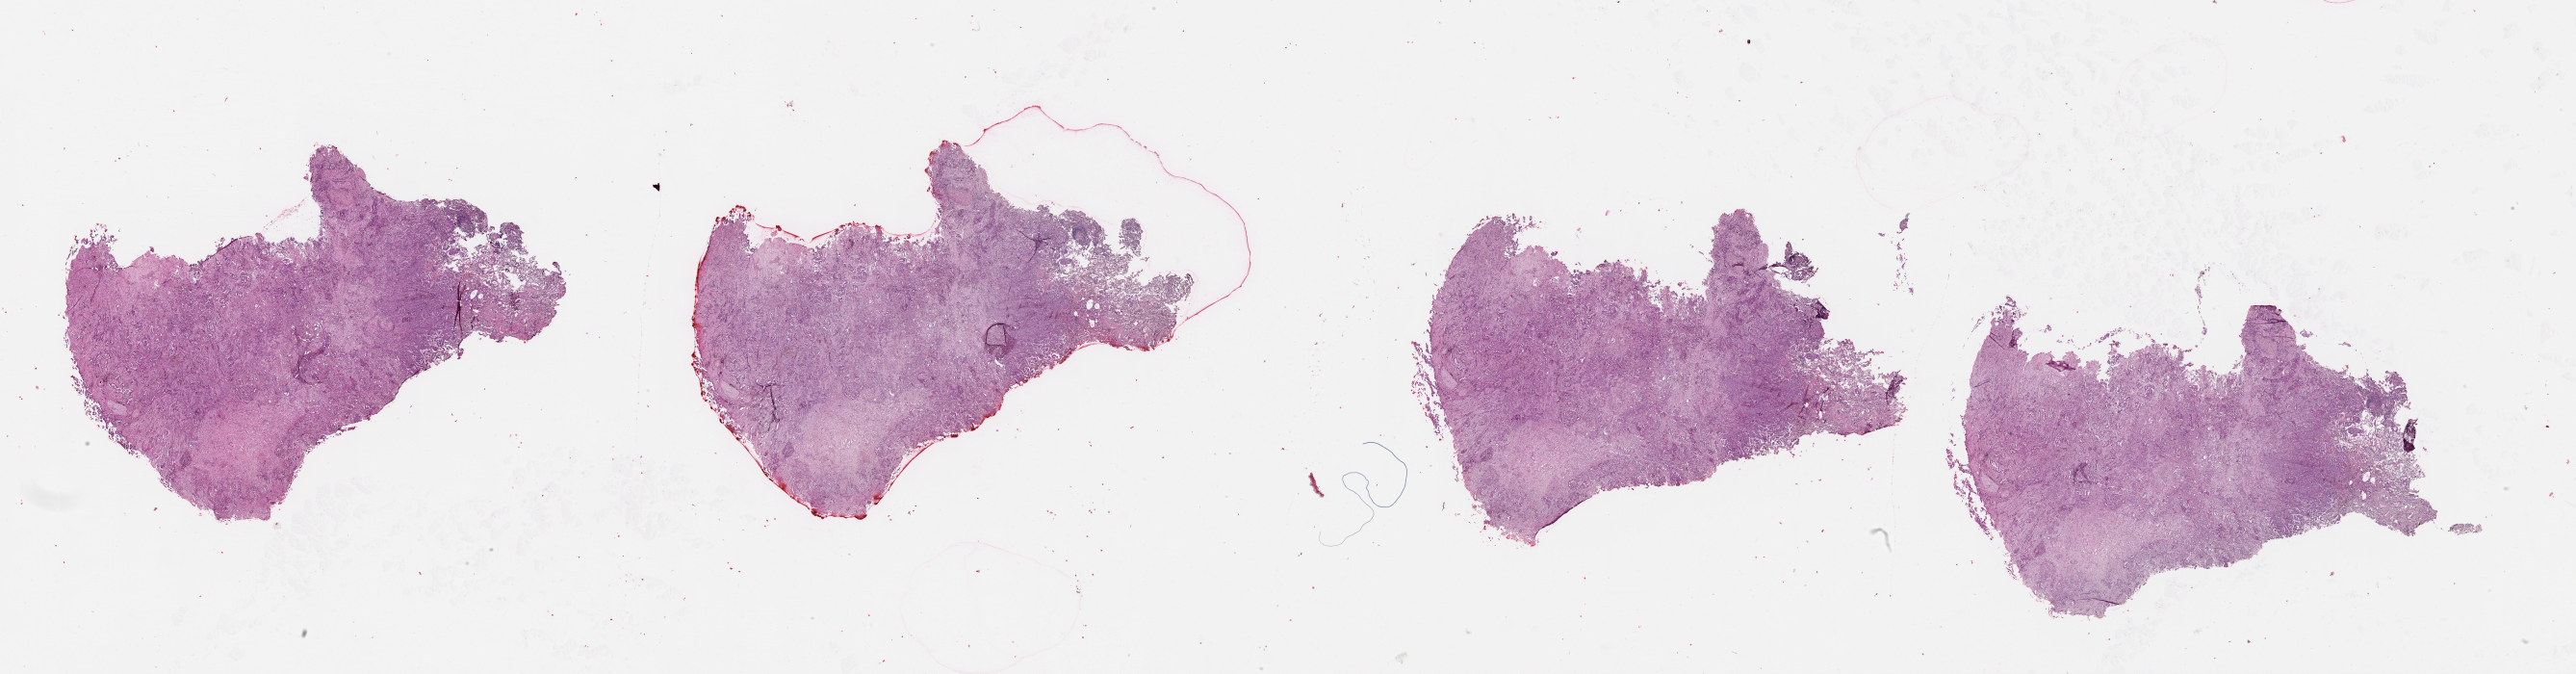
Whole-slide histology image, H&E, low-resolution overview of the scanned area, about 43.1 x 11.3 mm (slide scanned at 20x), lung, tissue type not recorded.
Patient diagnosis (cohort enrolment): lung adenocarcinoma (lung).